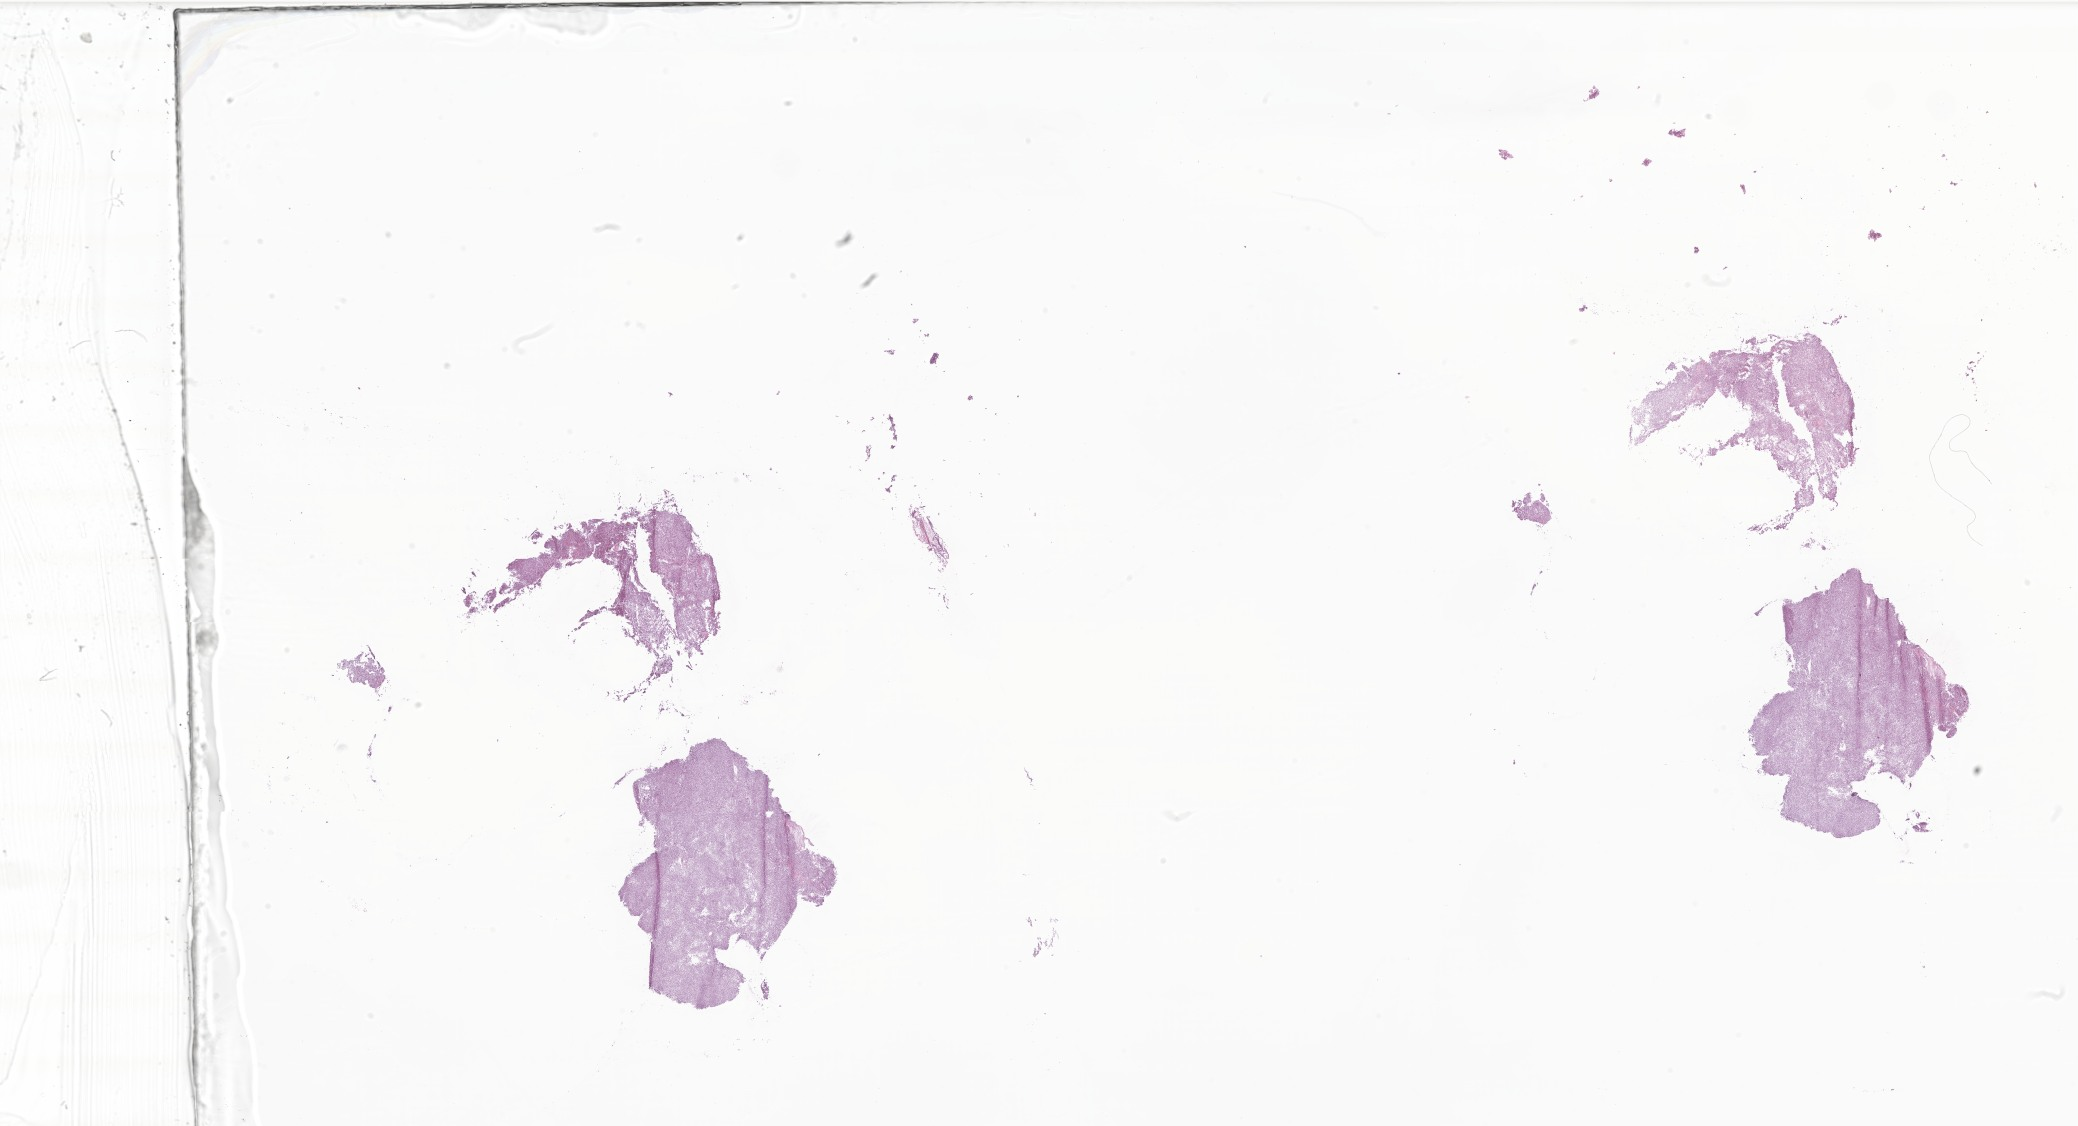
Hematoxylin and eosin (H&E) whole-slide image of tumor tissue from the occipital lobe, low-resolution overview of the scanned area, about 35.0 x 19.0 mm, frozen section (OCT-embedded). Male patient, age 148 months (12 years 4 months).
Diagnosis (ICD-O-3 morphology term): Glioma, malignant.